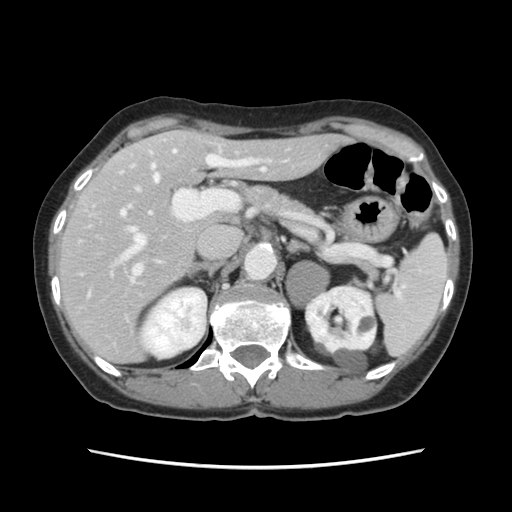
Contrast-enhanced abdominal CT, one axial slice. Position 79 of 120 along the scan axis. Intravenous contrast given. Soft-tissue window (W 400 / L 40 HU). 2.5 mm slice thickness. 512 × 512 image matrix, field of view 330 × 330 mm. Female patient, age 70 years. Case-level facts recorded for this patient, not image findings: diagnosis: colorectal cancer liver metastases, imaged before liver resection; multiple liver metastases: no; largest metastasis: 2.5 cm; disease in both lobes: no.
Outlined on this slice (manually delineated by an expert):
- hepatic veins: bounding box [x1, y1, x2, y2] px = [122, 150, 176, 260]
- liver: [59, 131, 339, 362]
- planned liver remnant (the part of the liver to remain after resection): [96, 131, 343, 285]
- portal vein (with intrahepatic branches): [120, 155, 271, 281]